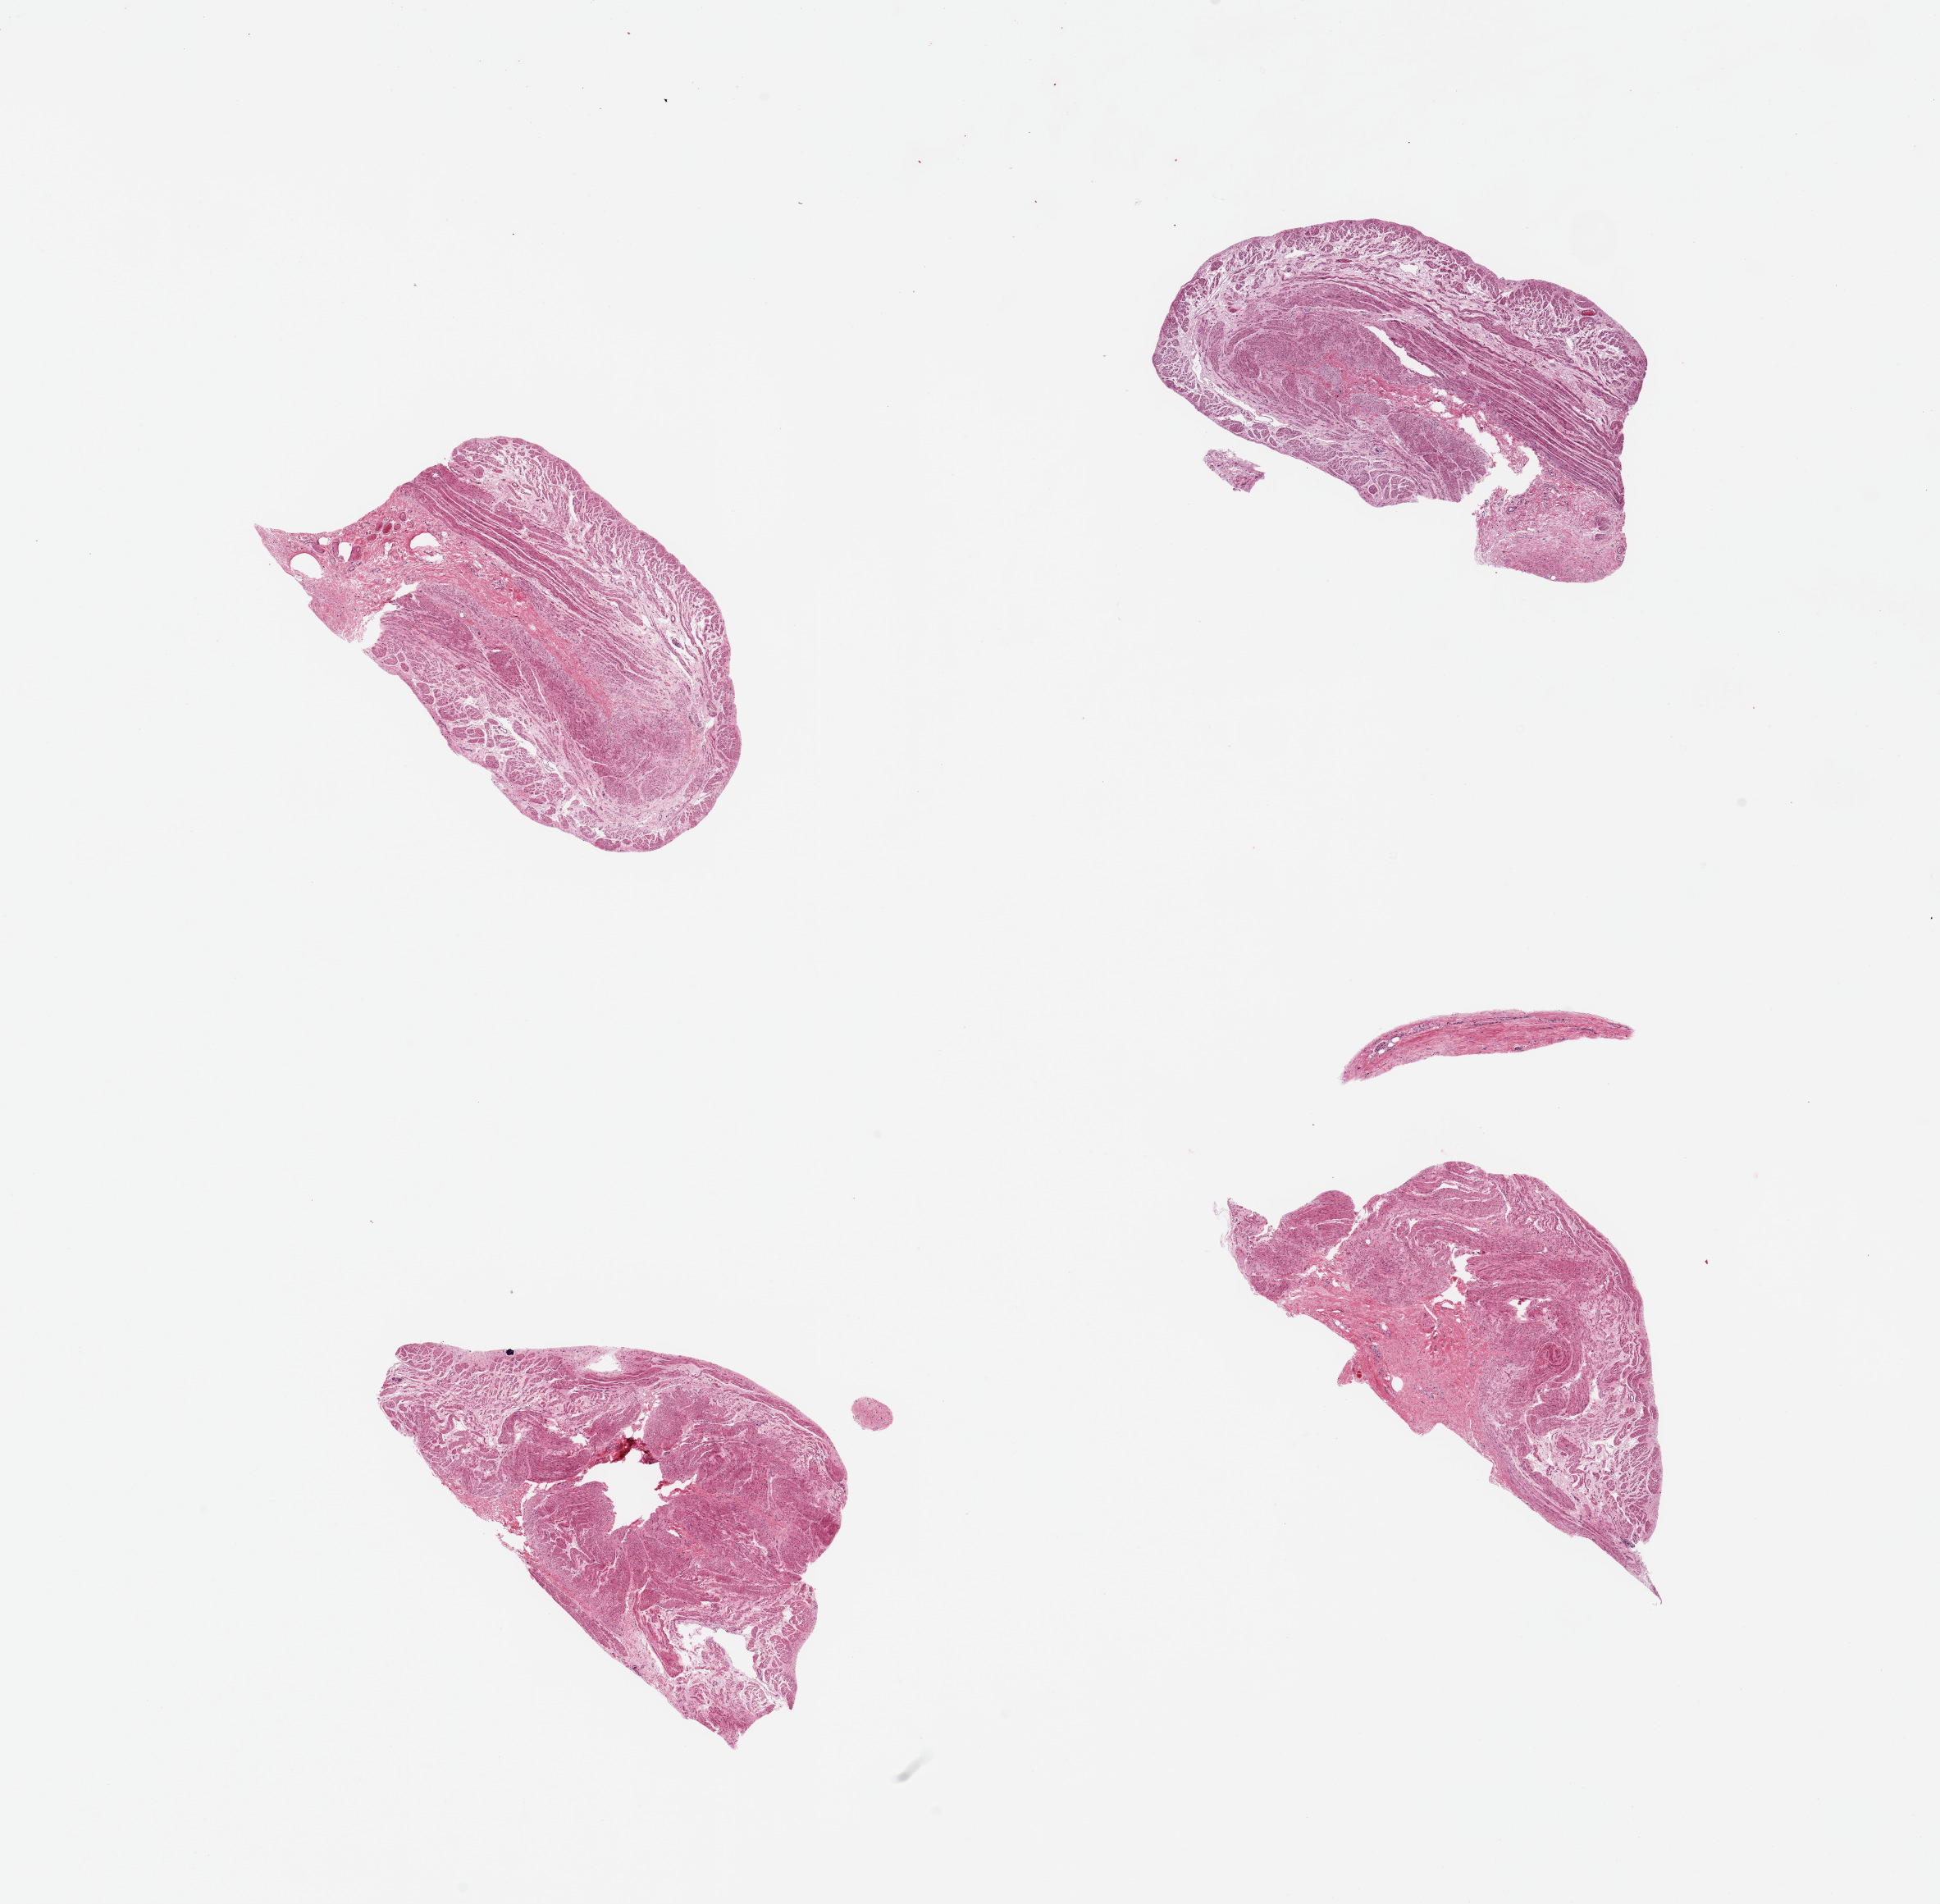
Hematoxylin and eosin (H&E) whole-slide image, brightfield, whole scanned area (about 18.7 x 18.4 mm) shown as a low-resolution overview; PAXgene-fixed paraffin-embedded (PFPE) section; sampled site (target tissue): stomach; tissue donor sample. Donor sex: male.
• reviewer comment on this tissue sample: 4 pieces; no mucosa, muscularis only